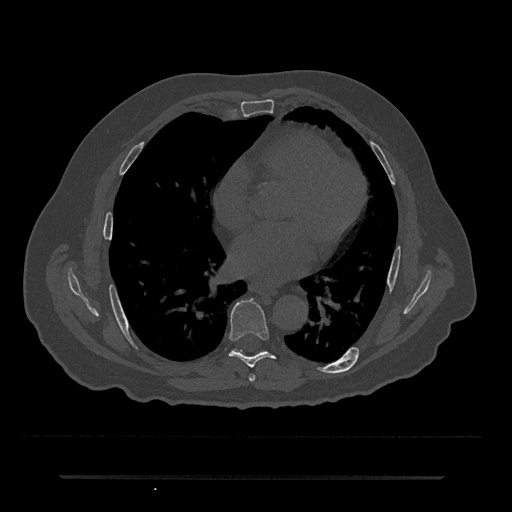
CT including the spine, one axial slice; position 378 of 797 along the scan axis; 120 kVp; bone window (W 1800 / L 400 HU); 0.5 mm slice thickness; 512 × 512 image matrix, field of view 437 × 437 mm. Patient: male, 69 years. Case-level facts recorded for this patient, not image findings: primary cancer: prostate.
Structures marked on this image (semi-automatically segmented with operator editing):
- T6 vertebra: box from (x=249, y=374) to (x=256, y=381) px
- T7 vertebra: (x=229, y=298)–(x=275, y=368)